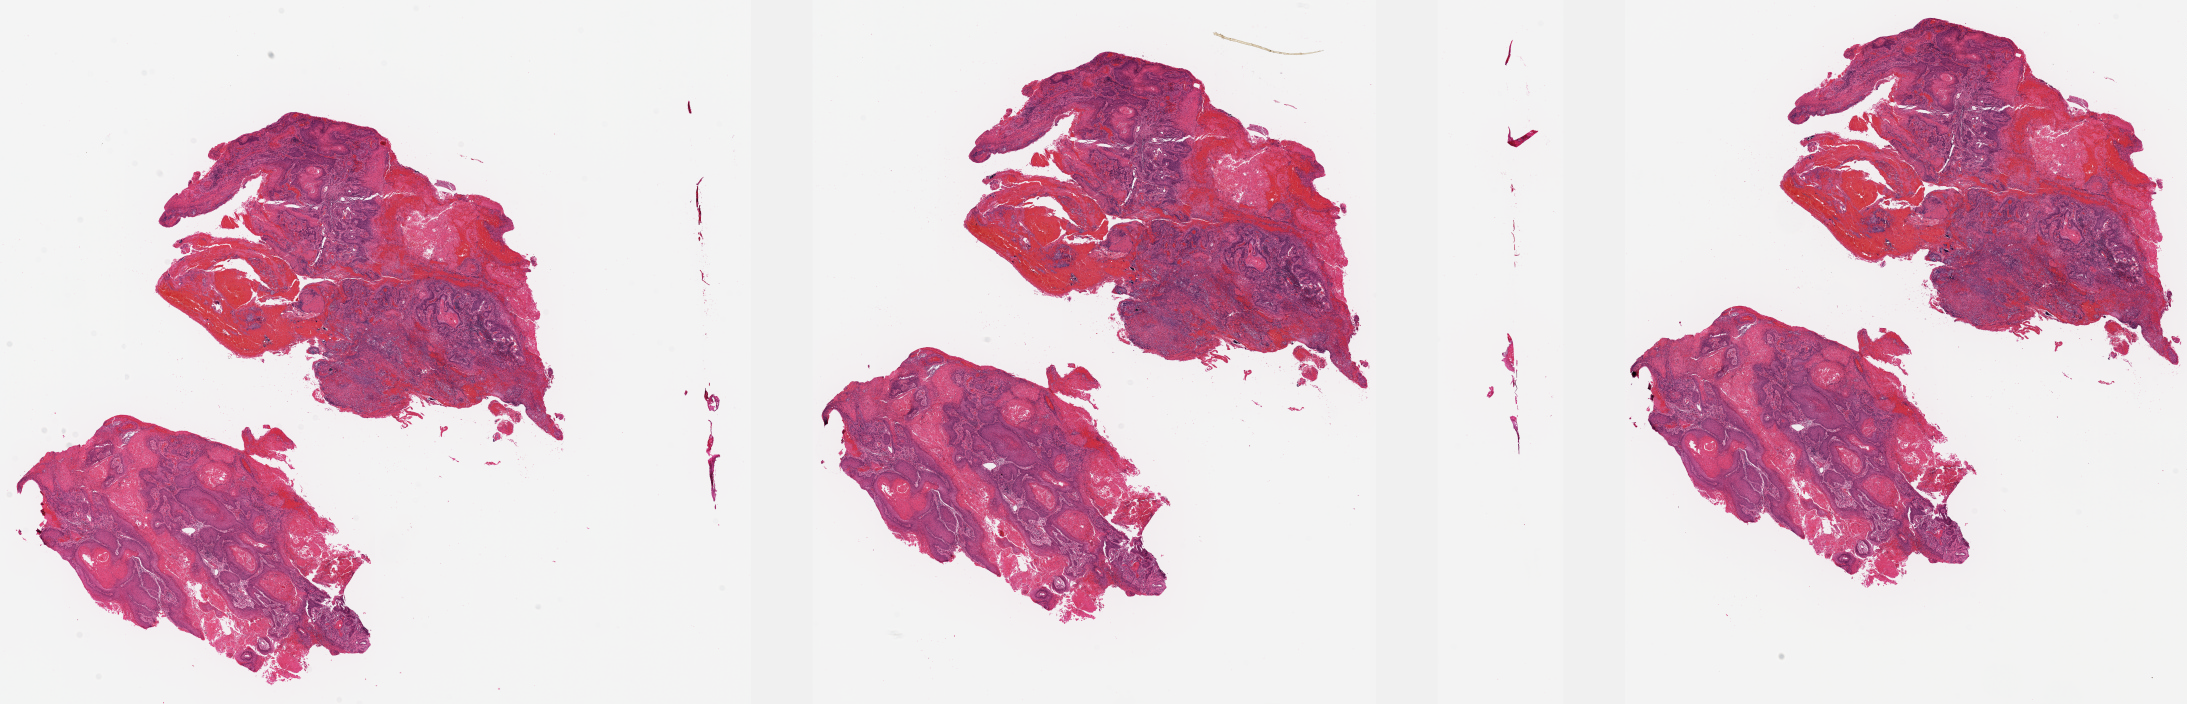
Whole-slide histology image, H&E-stained, shown as a low-resolution overview of the whole scanned area (about 34.6 x 11.1 mm, slide scanned at 20x), formalin-fixed paraffin-embedded (FFPE) diagnostic section, head and neck, primary tumour sample. Male patient; age at initial diagnosis 72 years. Histologic grade: G1 (well differentiated).
AJCC pathologic stage: IVA (7th edition). Pathologic diagnosis: Squamous cell carcinoma, NOS (cheek mucosa).